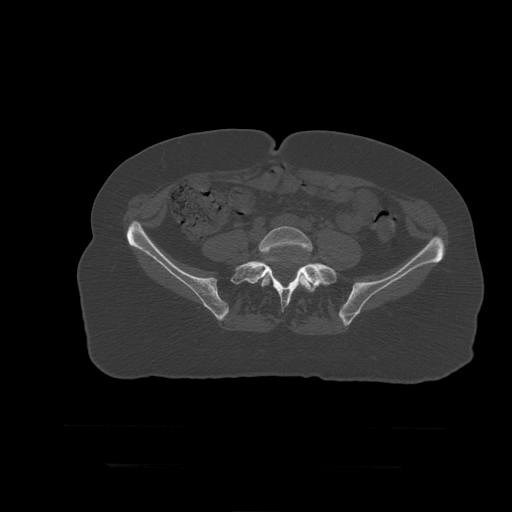
CT including the spine, one axial slice. Slice 61 of 399 in the series (ordered by position). Reconstruction kernel STANDARD. Bone window (W 1800 / L 400 HU). 512 × 512 image matrix, field of view 450 × 450 mm. Patient age 41 years. Case-level facts recorded for this patient, not image findings: primary cancer: breast.
Outlined on this slice (semi-automatic segmentation, software-assisted and operator-edited):
- L5 vertebra: bounding box [x1, y1, x2, y2] px = [259, 227, 317, 293]